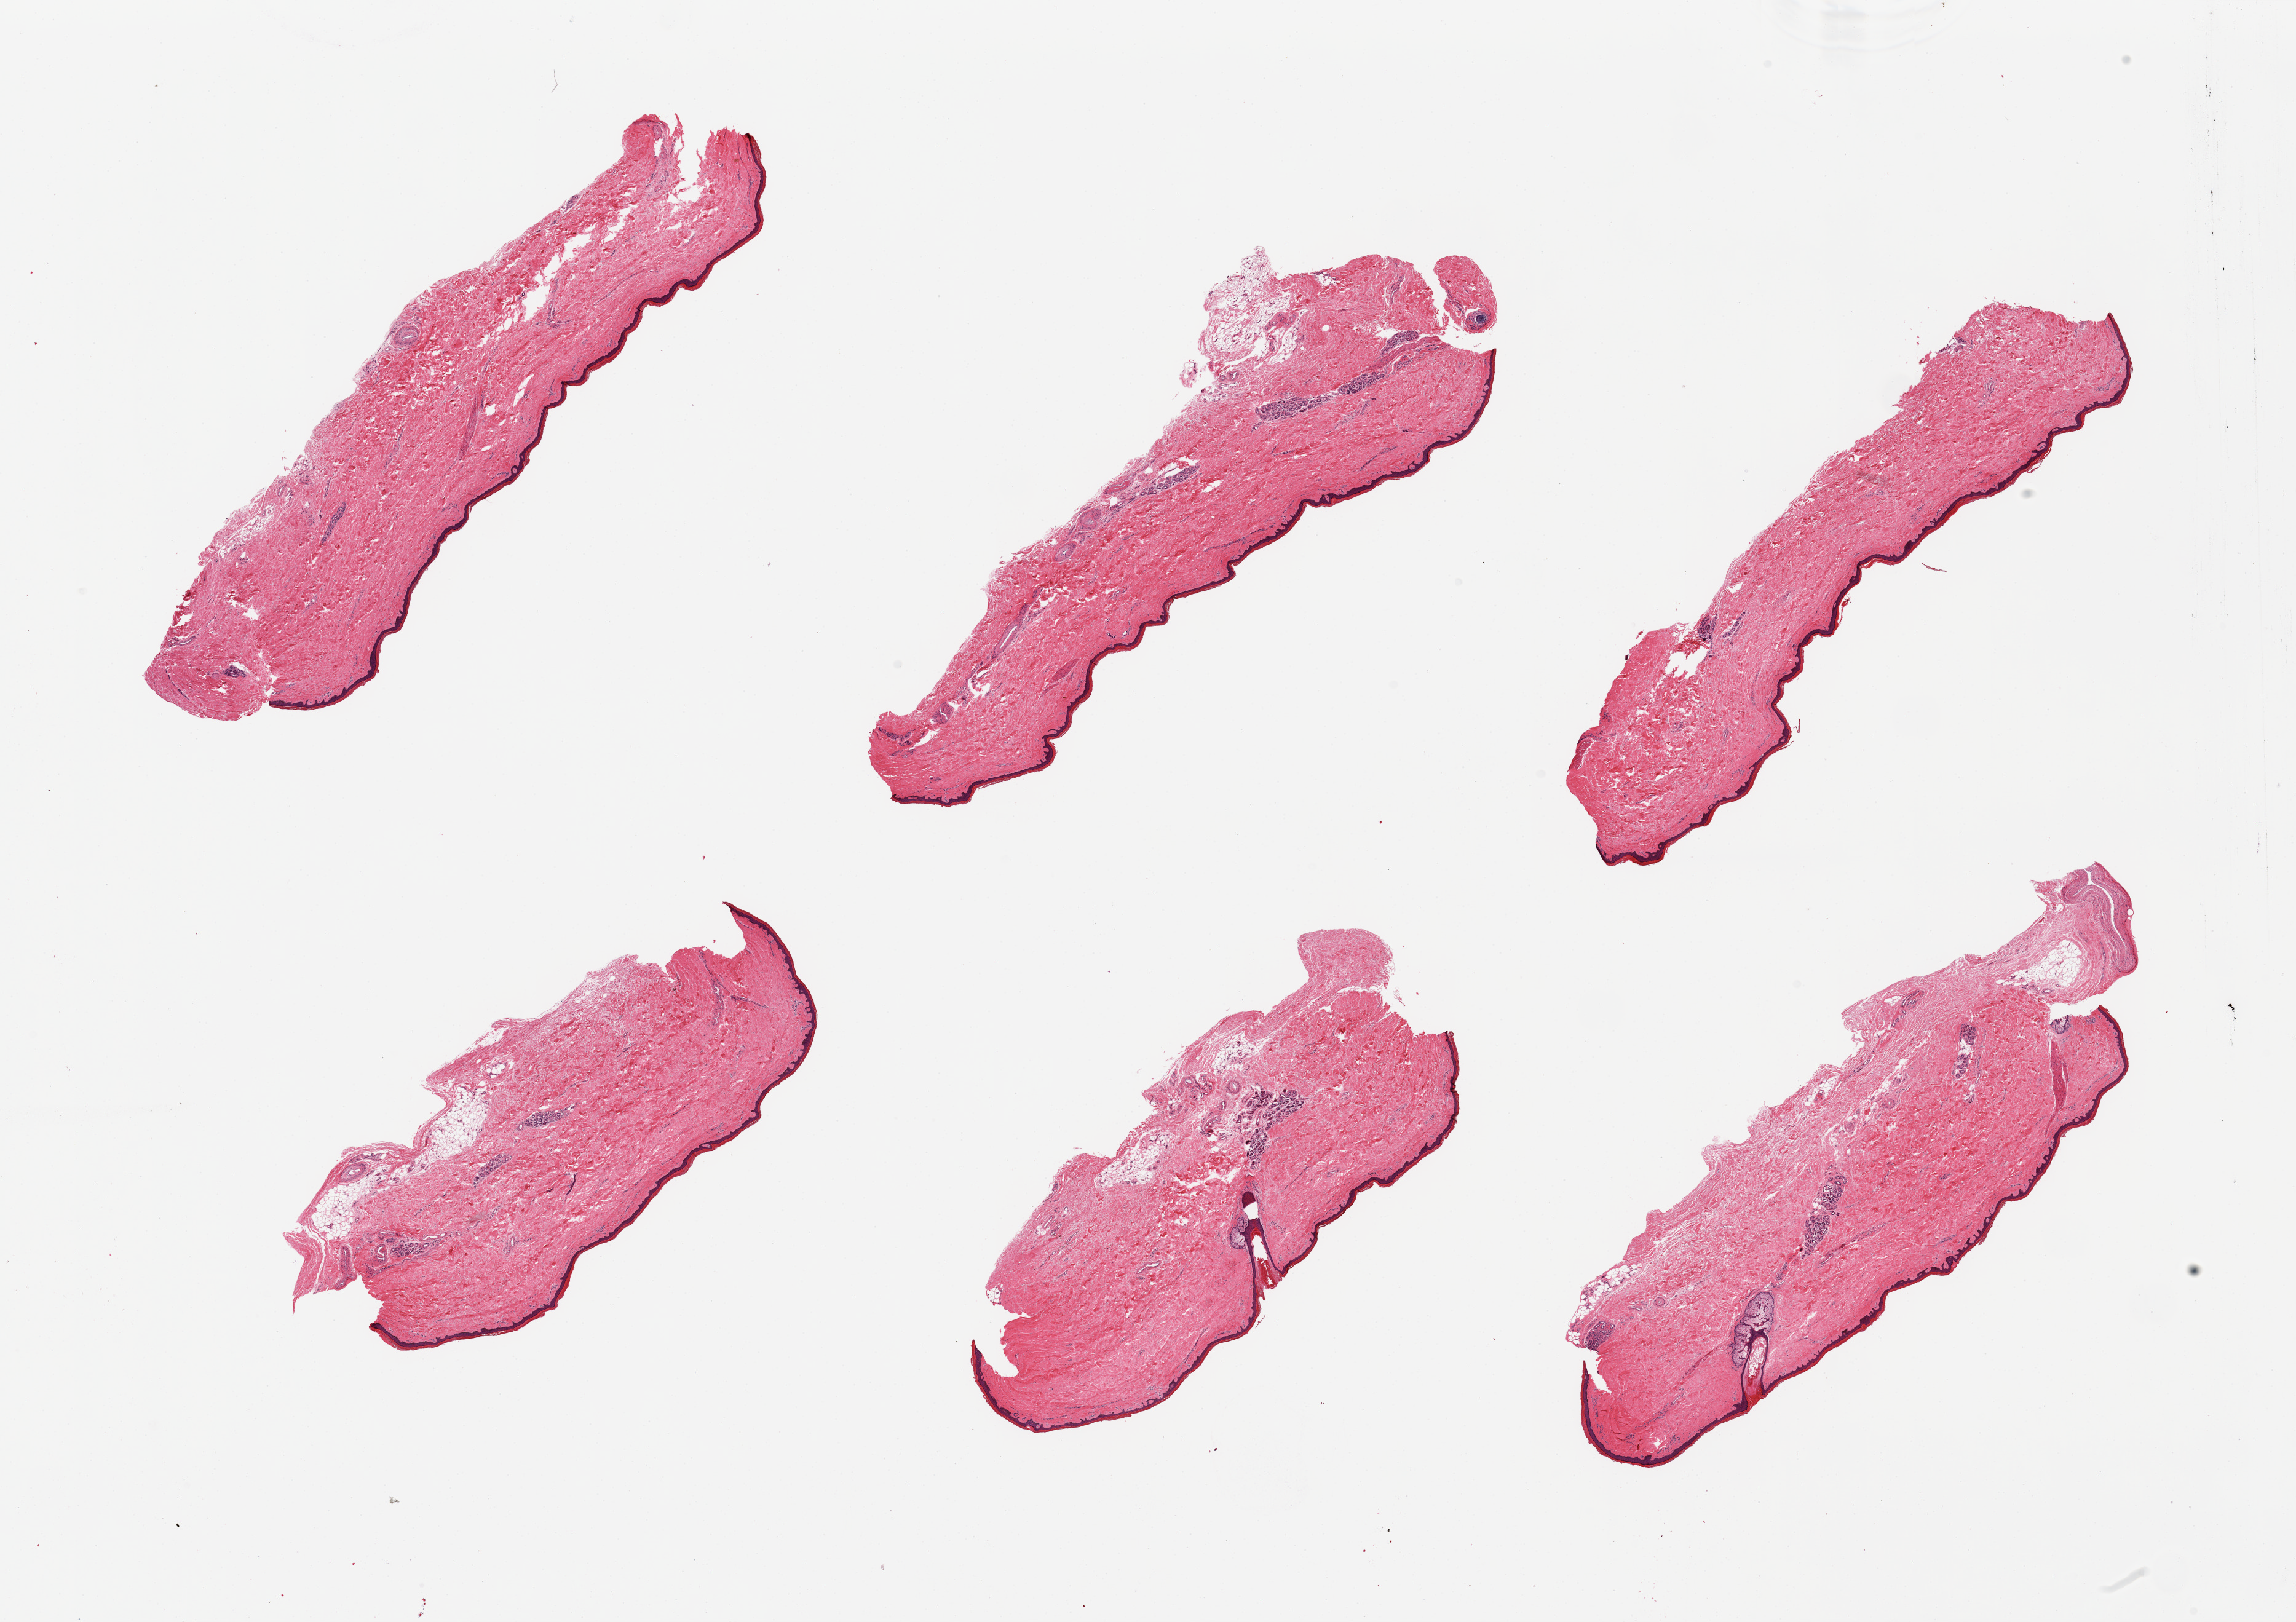
Haematoxylin and eosin whole-slide image — shown as a low-resolution overview of the whole scanned area (about 29.5 x 20.9 mm, acquisition: 20x scan), PAXgene-fixed, paraffin-embedded tissue, target tissue: skin of lower leg, tissue donor sample. Donor sex: male.
Reviewer comment on this tissue sample: 6 pieces; well trimmed, the epidermis measures 33 to 53 microns.